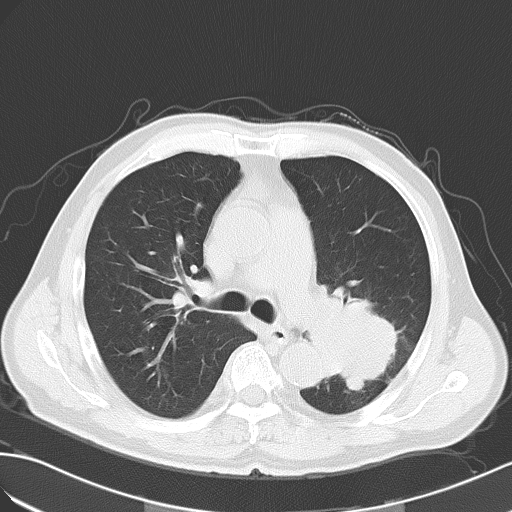
Chest CT, one axial slice; position 35 of 55 along the scan axis; reconstruction kernel B70f; 120 kVp; lung window (W 1500 / L -600 HU); 5 mm slice thickness; 512 × 512 image matrix. Male patient, age 63 years. From the clinical record (not read from this slice): clinical TNM (as recorded): T3 N3 M1a.
Structures marked on this image (rectangle marked by the reading radiologist):
- lung tumour (recorded histology: large cell carcinoma): box from (x=313, y=280) to (x=410, y=404) px